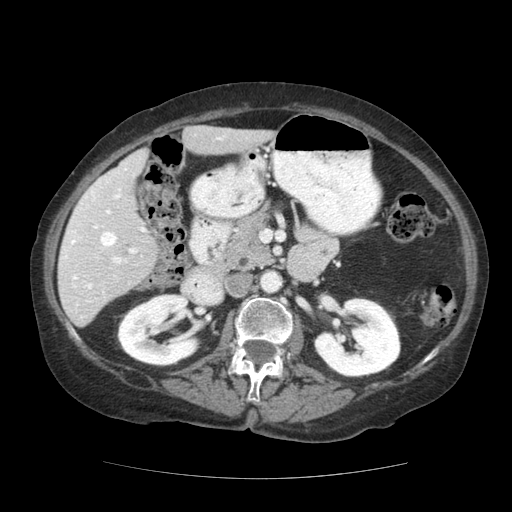
Contrast-enhanced abdominal CT (liver protocol), one axial slice. Reconstruction kernel STANDARD. Soft-tissue window (W 400 / L 40 HU). 2.5 mm slice thickness. 512 × 512 image matrix, field of view 360 × 360 mm. From the clinical record (not read from this slice): diagnosis: hepatocellular carcinoma (patient treated with transarterial chemoembolisation; whether this scan precedes or follows treatment is not stated here); TNM stage (as recorded): Stage-I; Child-Pugh class: A; tumour differentiation: moderately-poorly differentiated; tumour nodularity: uninodular.
Structures marked on this image (semi-automatically segmented with operator editing):
- liver parenchyma outside the tumour (the mass and vessels are separate outlines, so this box may not span the whole liver): bounding box (x1, y1, x2, y2) in pixels: (58, 126, 274, 326)
- liver vessels: (61, 137, 222, 289)